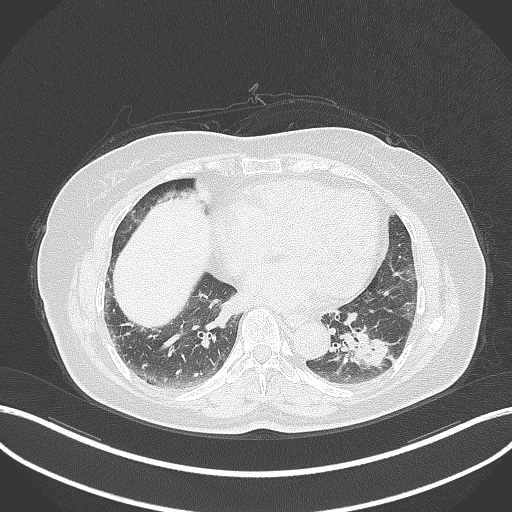
Chest CT, one axial slice. Slice 142 of 311 in the series (ordered by position). 120 kVp. Lung window (W 1500 / L -600 HU). 1 mm slice thickness. 512 × 512 image matrix, field of view 400 × 400 mm. Female patient, age 59 years. Case-level facts recorded for this patient, not image findings: clinical TNM (as recorded): T2a N0 M0; histopathological grade: G2-3.
Annotated regions visible in this slice (bounding box drawn by a radiologist):
- lung tumour (recorded histology: adenocarcinoma): box from (x=334, y=325) to (x=394, y=371) px